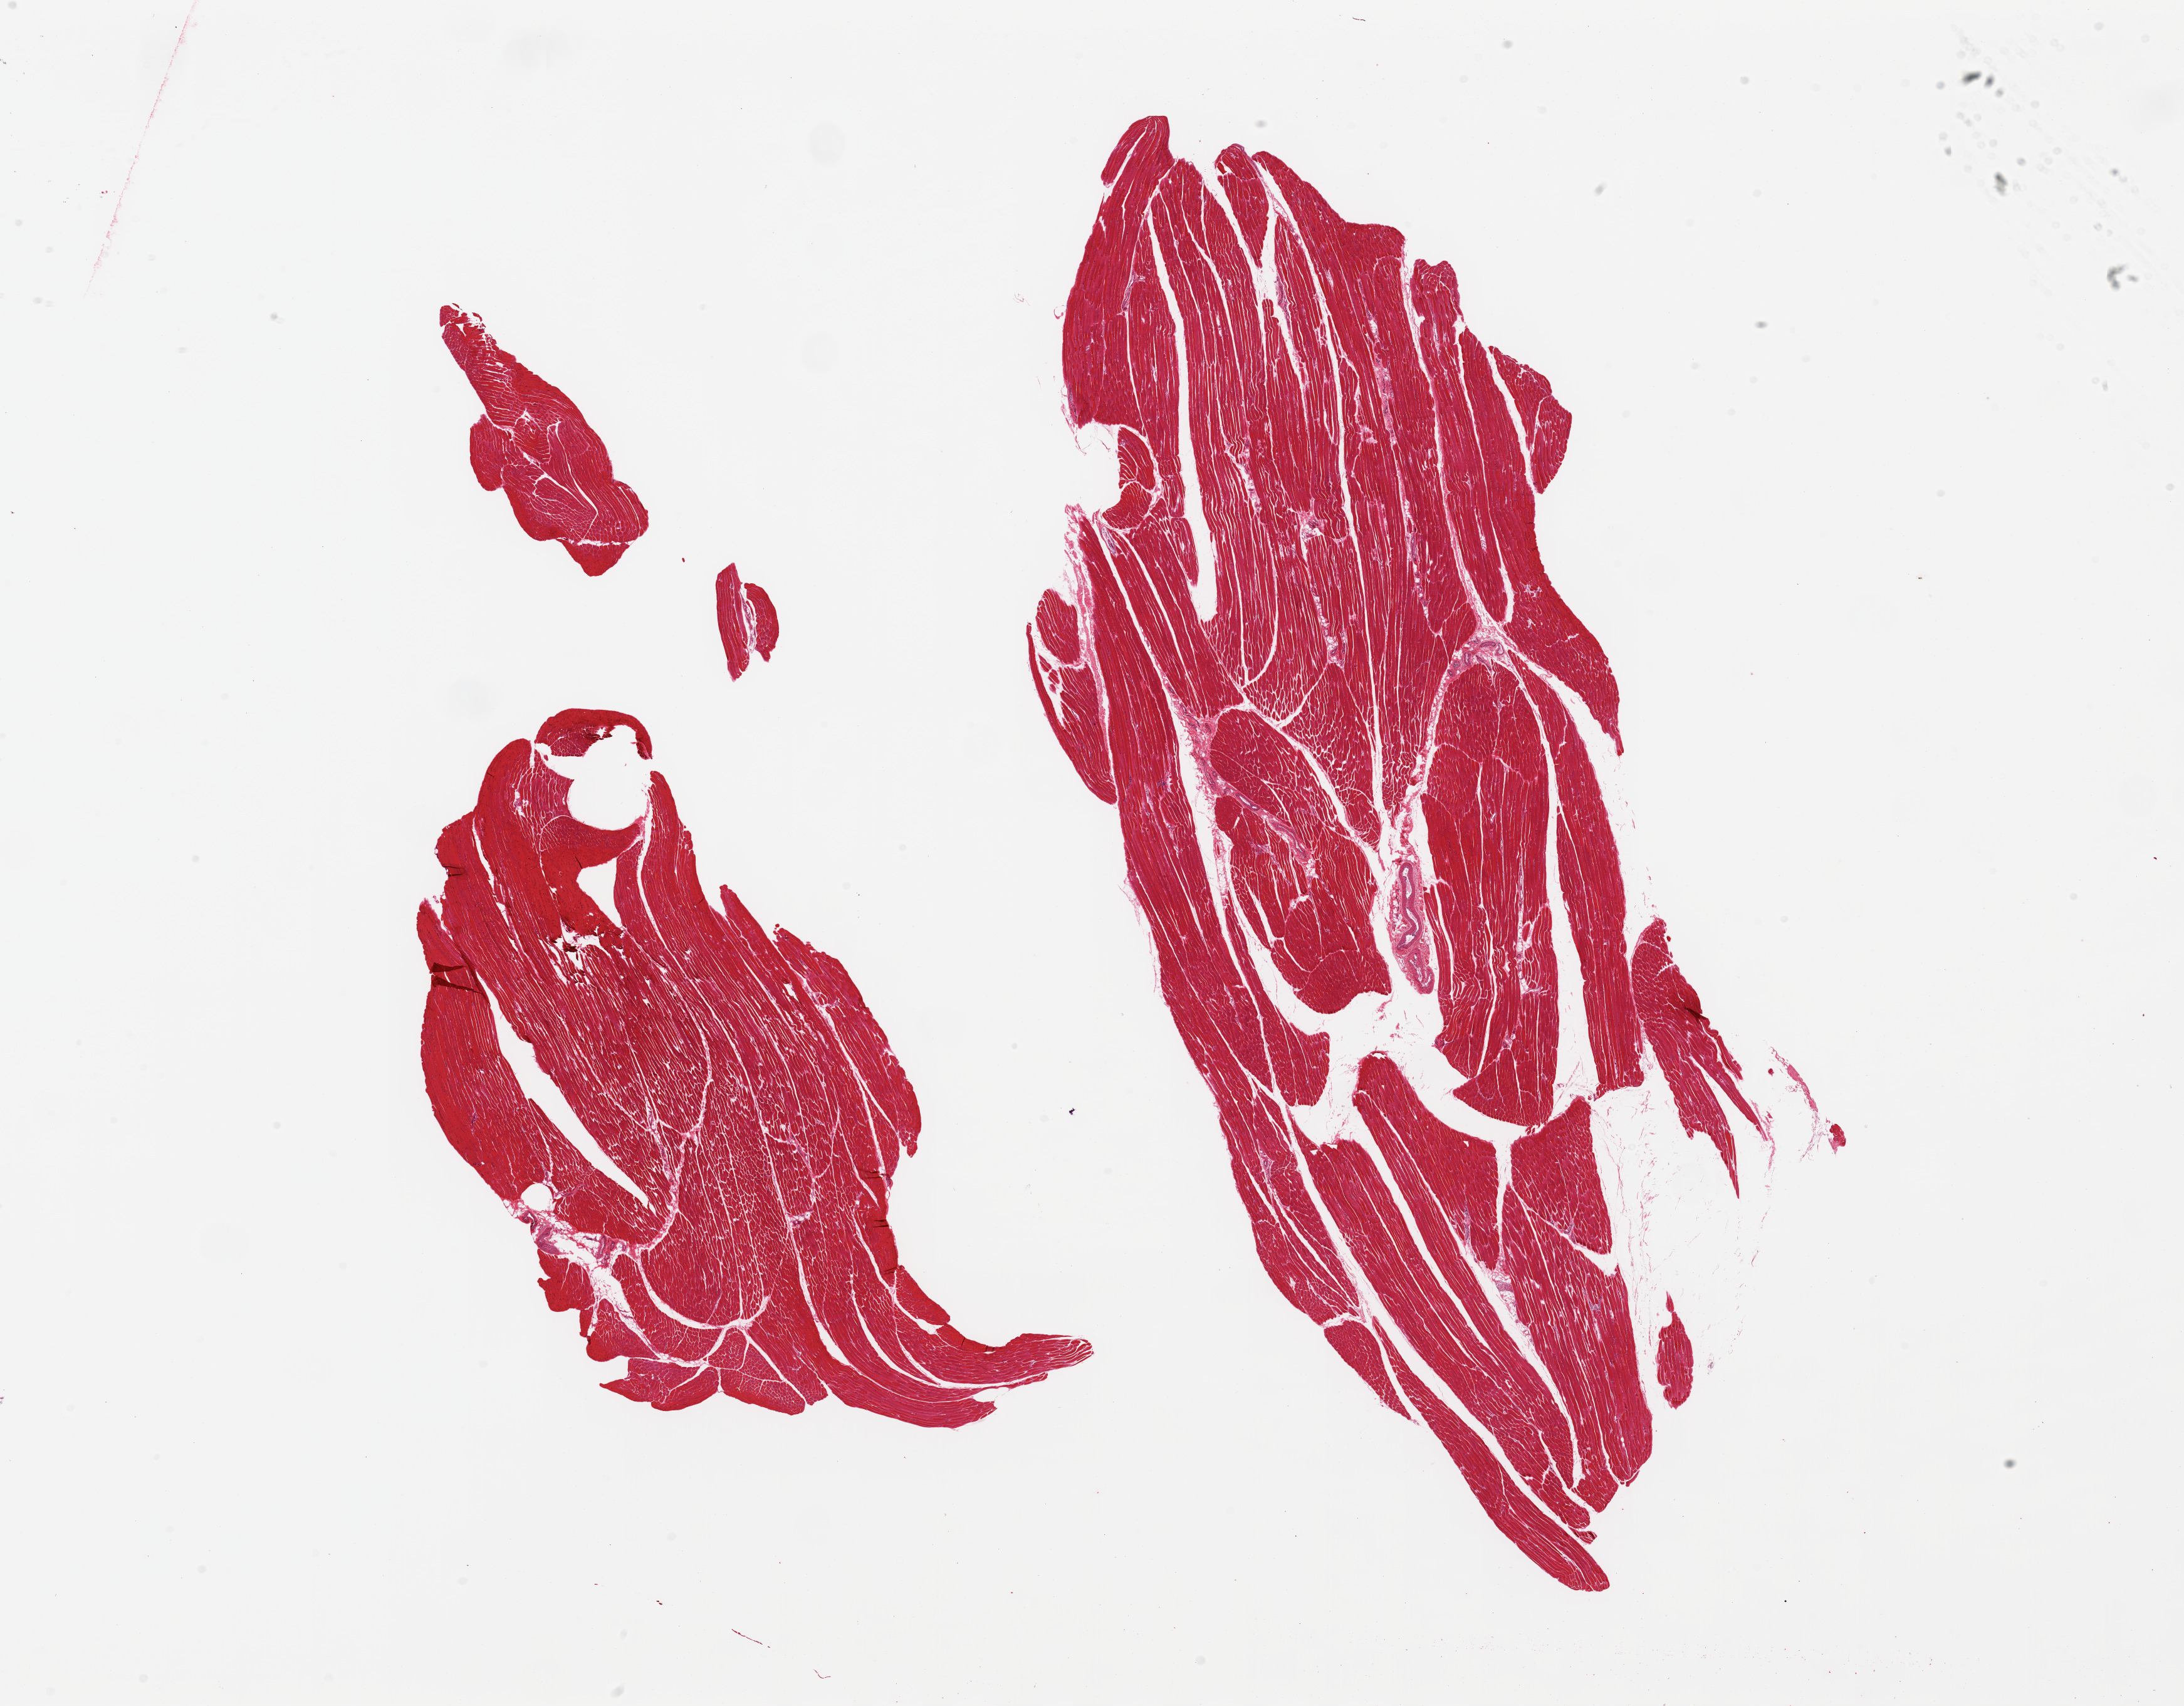
Whole-slide image, hematoxylin and eosin (H&E) stain, brightfield, low-resolution overview of the scanned area, about 27.6 x 21.5 mm (slide scanned at 20x). PAXgene-fixed paraffin-embedded (PFPE) section. Section of skeletal muscle (target tissue). Tissue donor sample. Donor sex: female.
Review note (as recorded): 2 pieces.